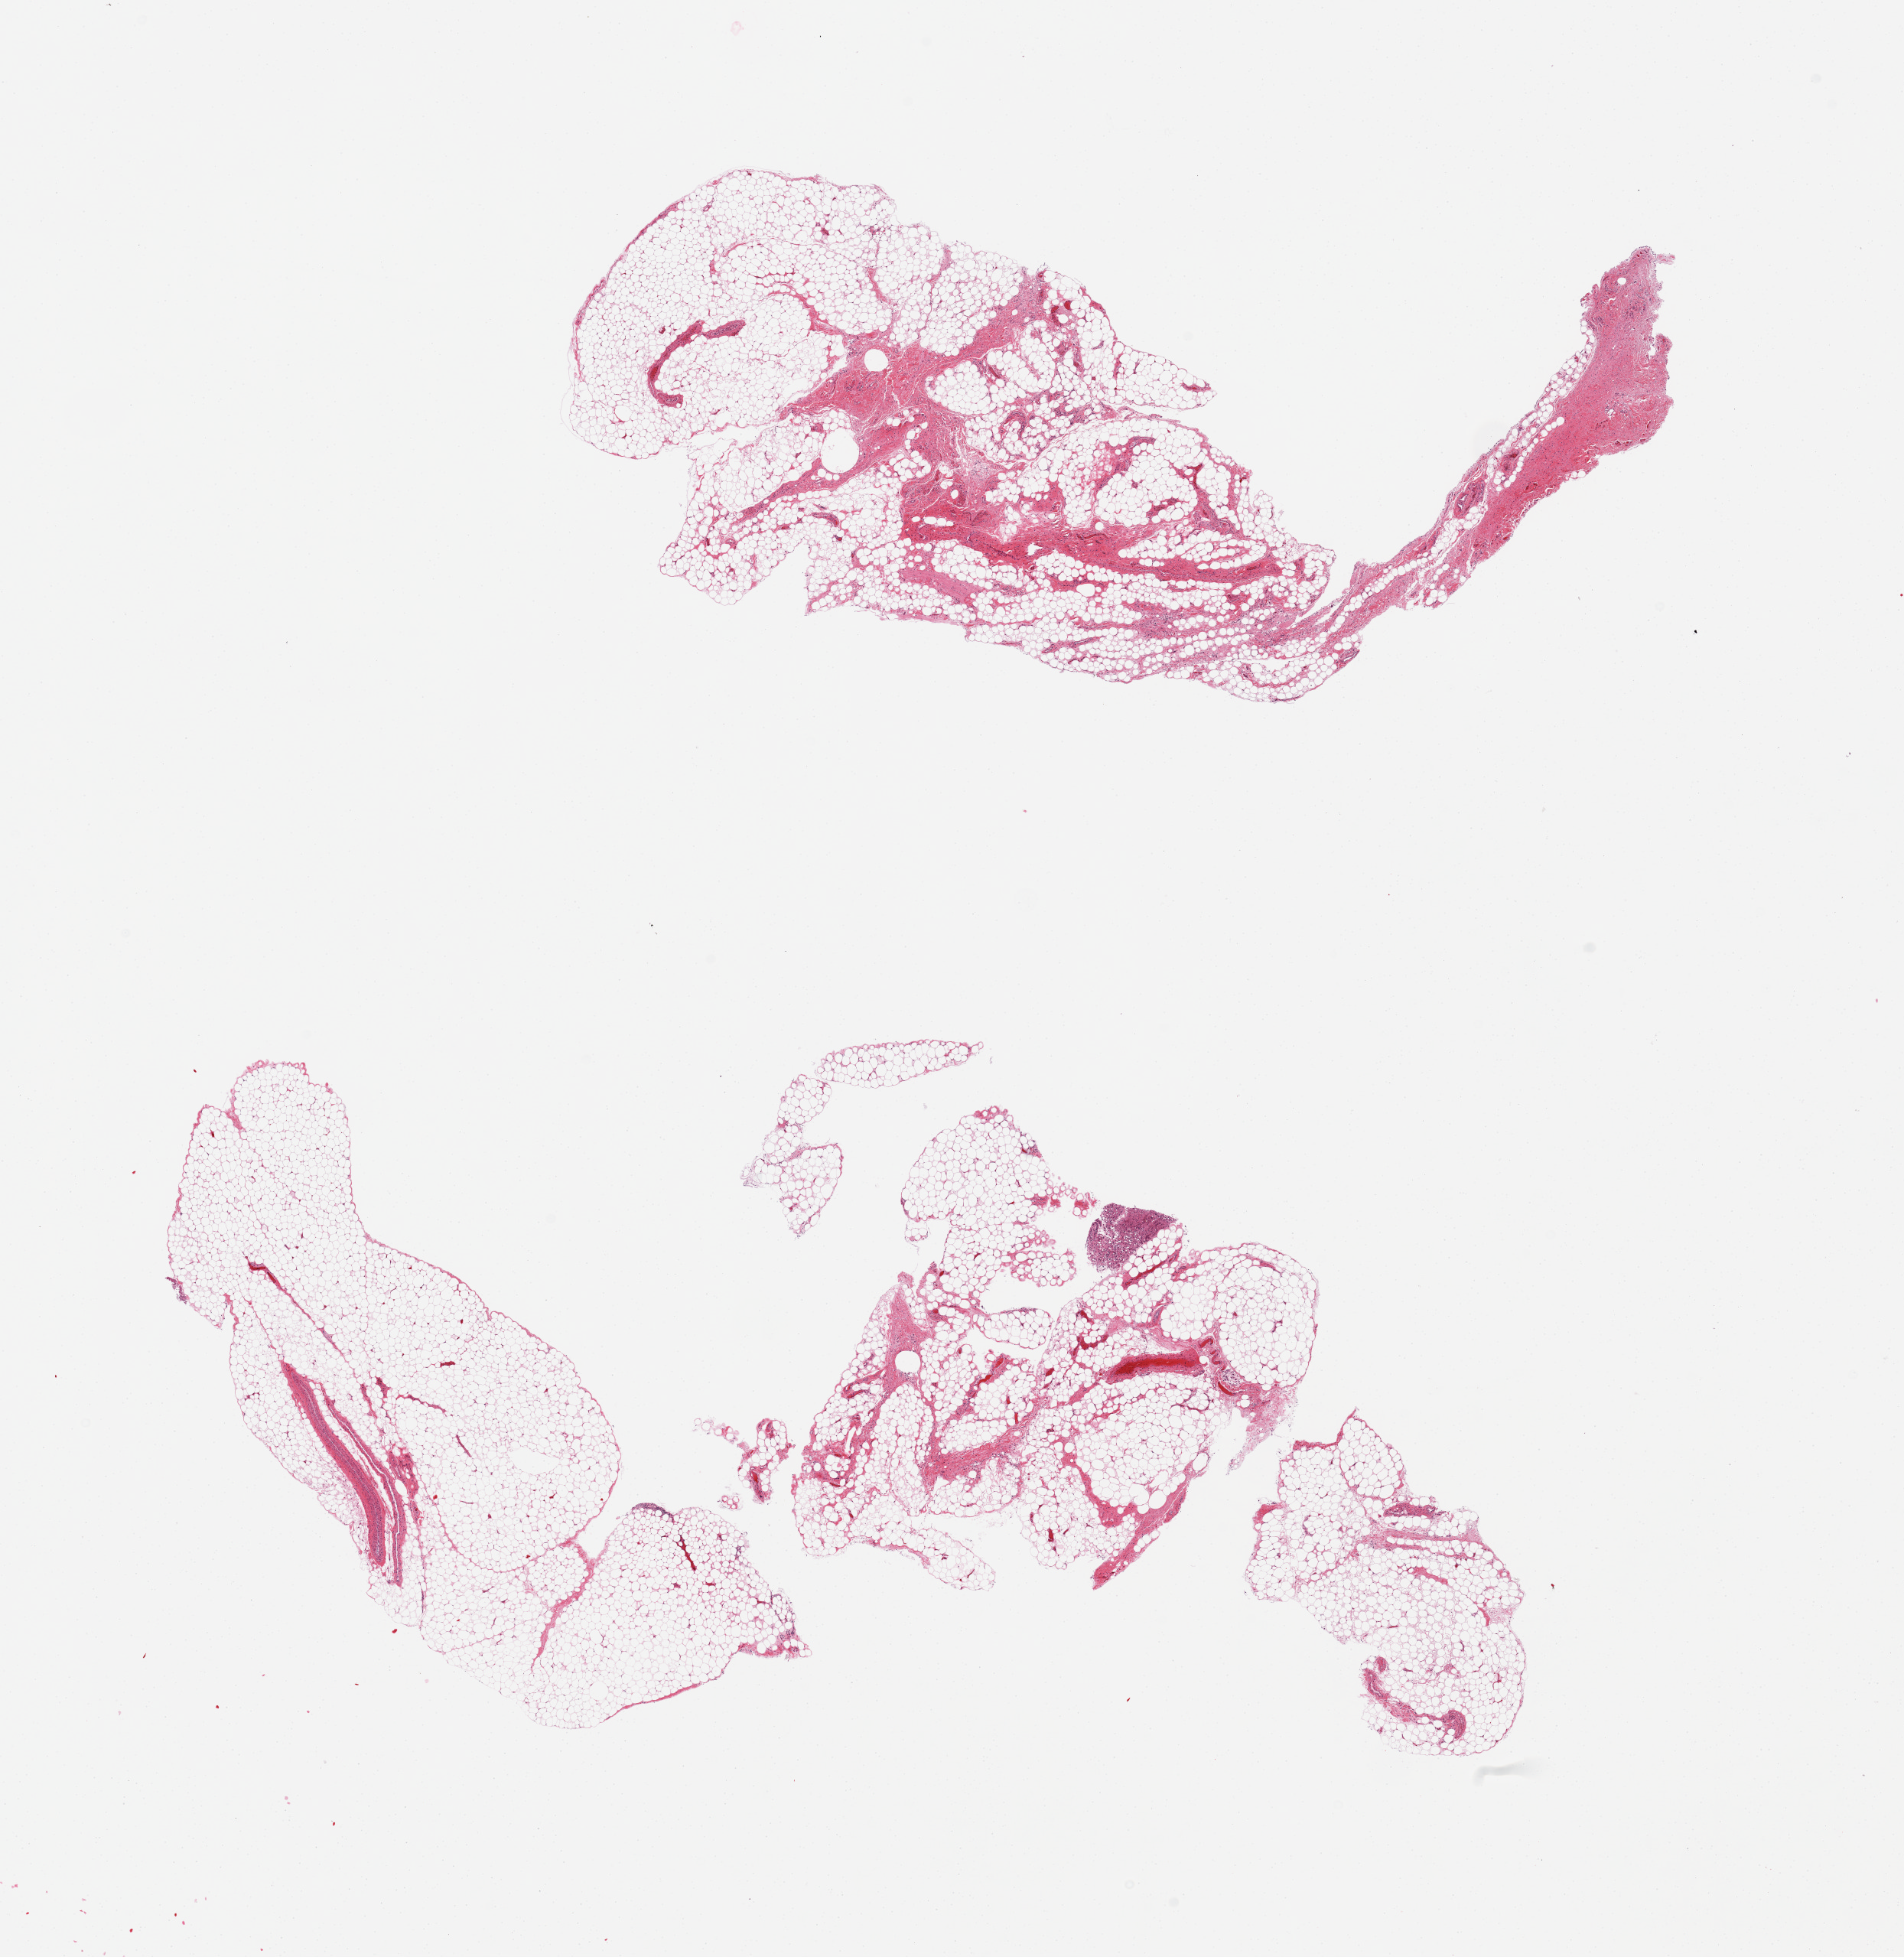
H&E whole-slide image — a low-resolution overview of the entire scanned area, about 19.7 x 20.2 mm; PAXgene-fixed, paraffin-embedded tissue; target tissue: omentum; tissue donor sample. Male donor.
• review note (as recorded): 2 pieces, 10% fibrous/vascular, includes small portion of autolyzed adrenal